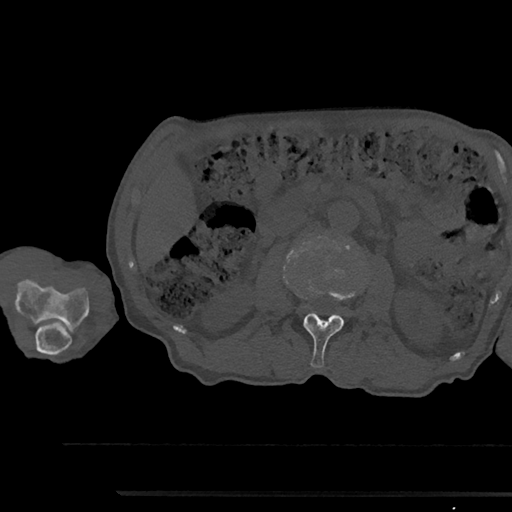
CT including the spine, one axial slice; slice 540 of 797 in the series (ordered by position); reconstruction kernel Br40s/3; 120 kVp; bone window (W 1800 / L 400 HU); 0.5 mm slice thickness; 512 × 512 image matrix, field of view 367 × 367 mm. Patient: male, 79 years. Case-level facts recorded for this patient, not image findings: primary cancer: prostate.
Outlined on this slice (semi-automatically segmented with operator editing):
- L2 vertebra: bounding box <303,289,355,368> (left, top, right, bottom; pixels)